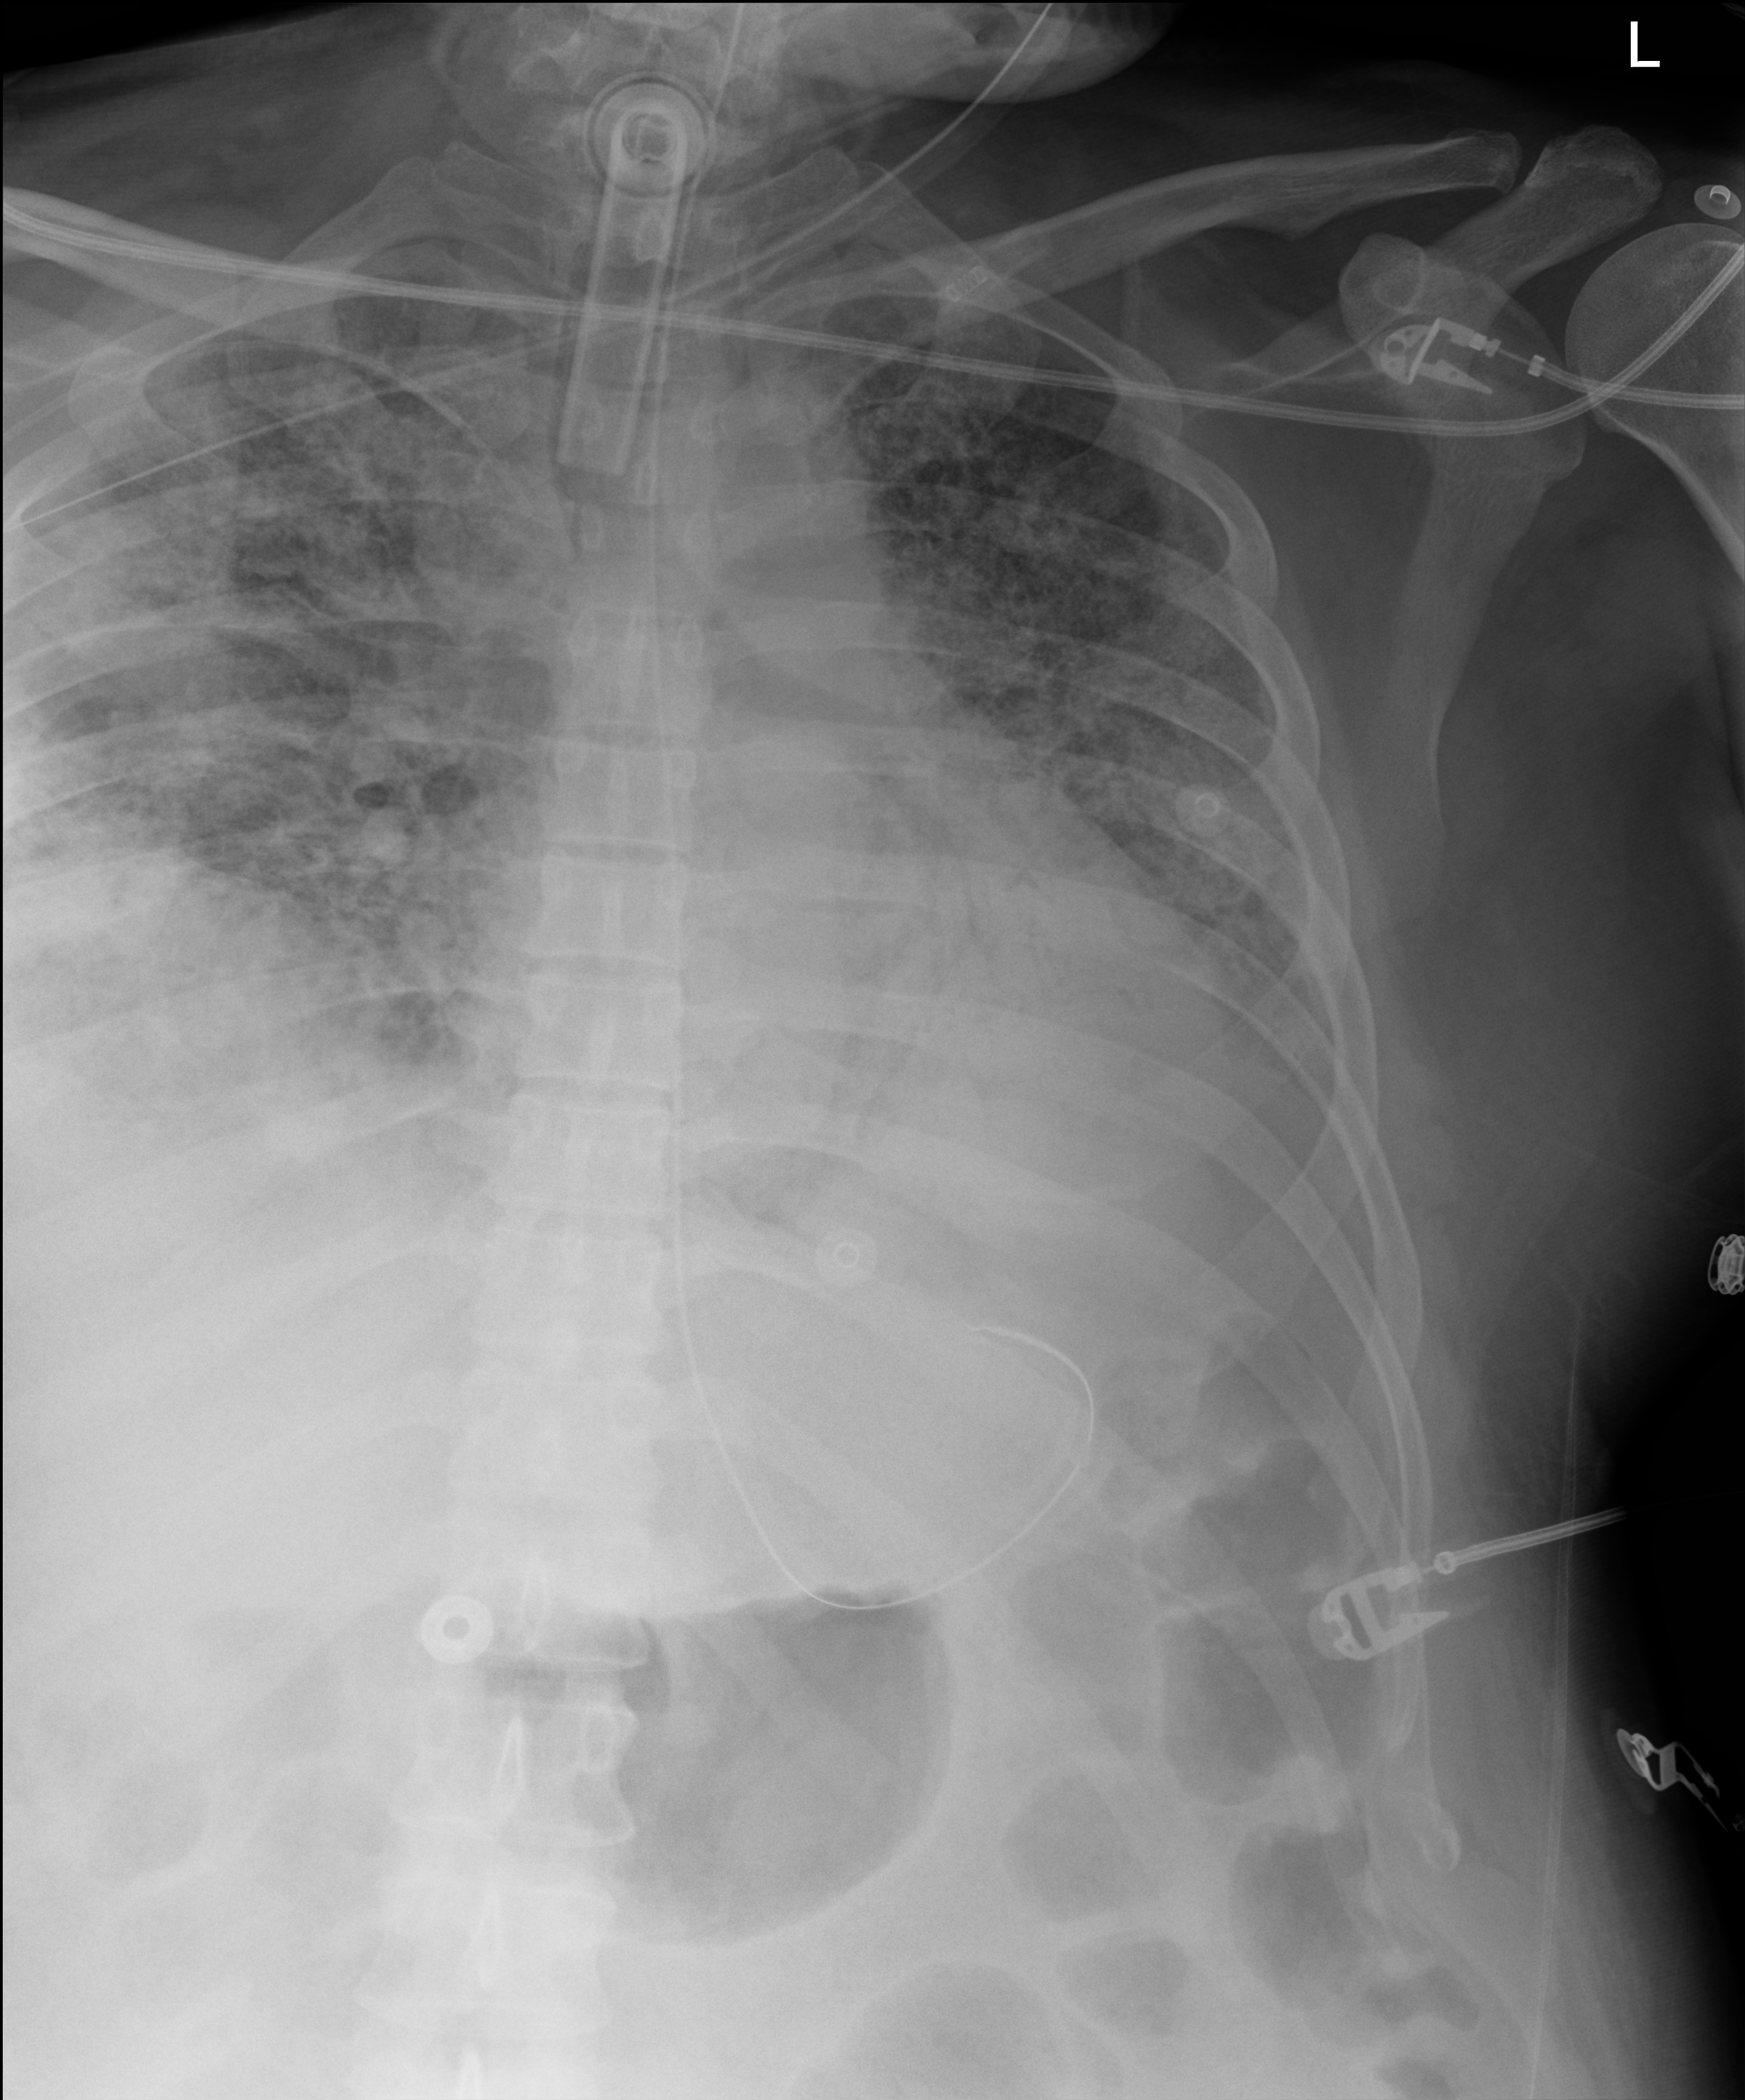
Bedside chest radiograph (digital radiography), anteroposterior (AP) projection. Patient hospitalised with COVID-19; male, aged 18–59 years.
Hospital-stay facts (about this admission, not read from this image; timing relative to this image not recorded):
- admitted to intensive care during this hospital stay: yes